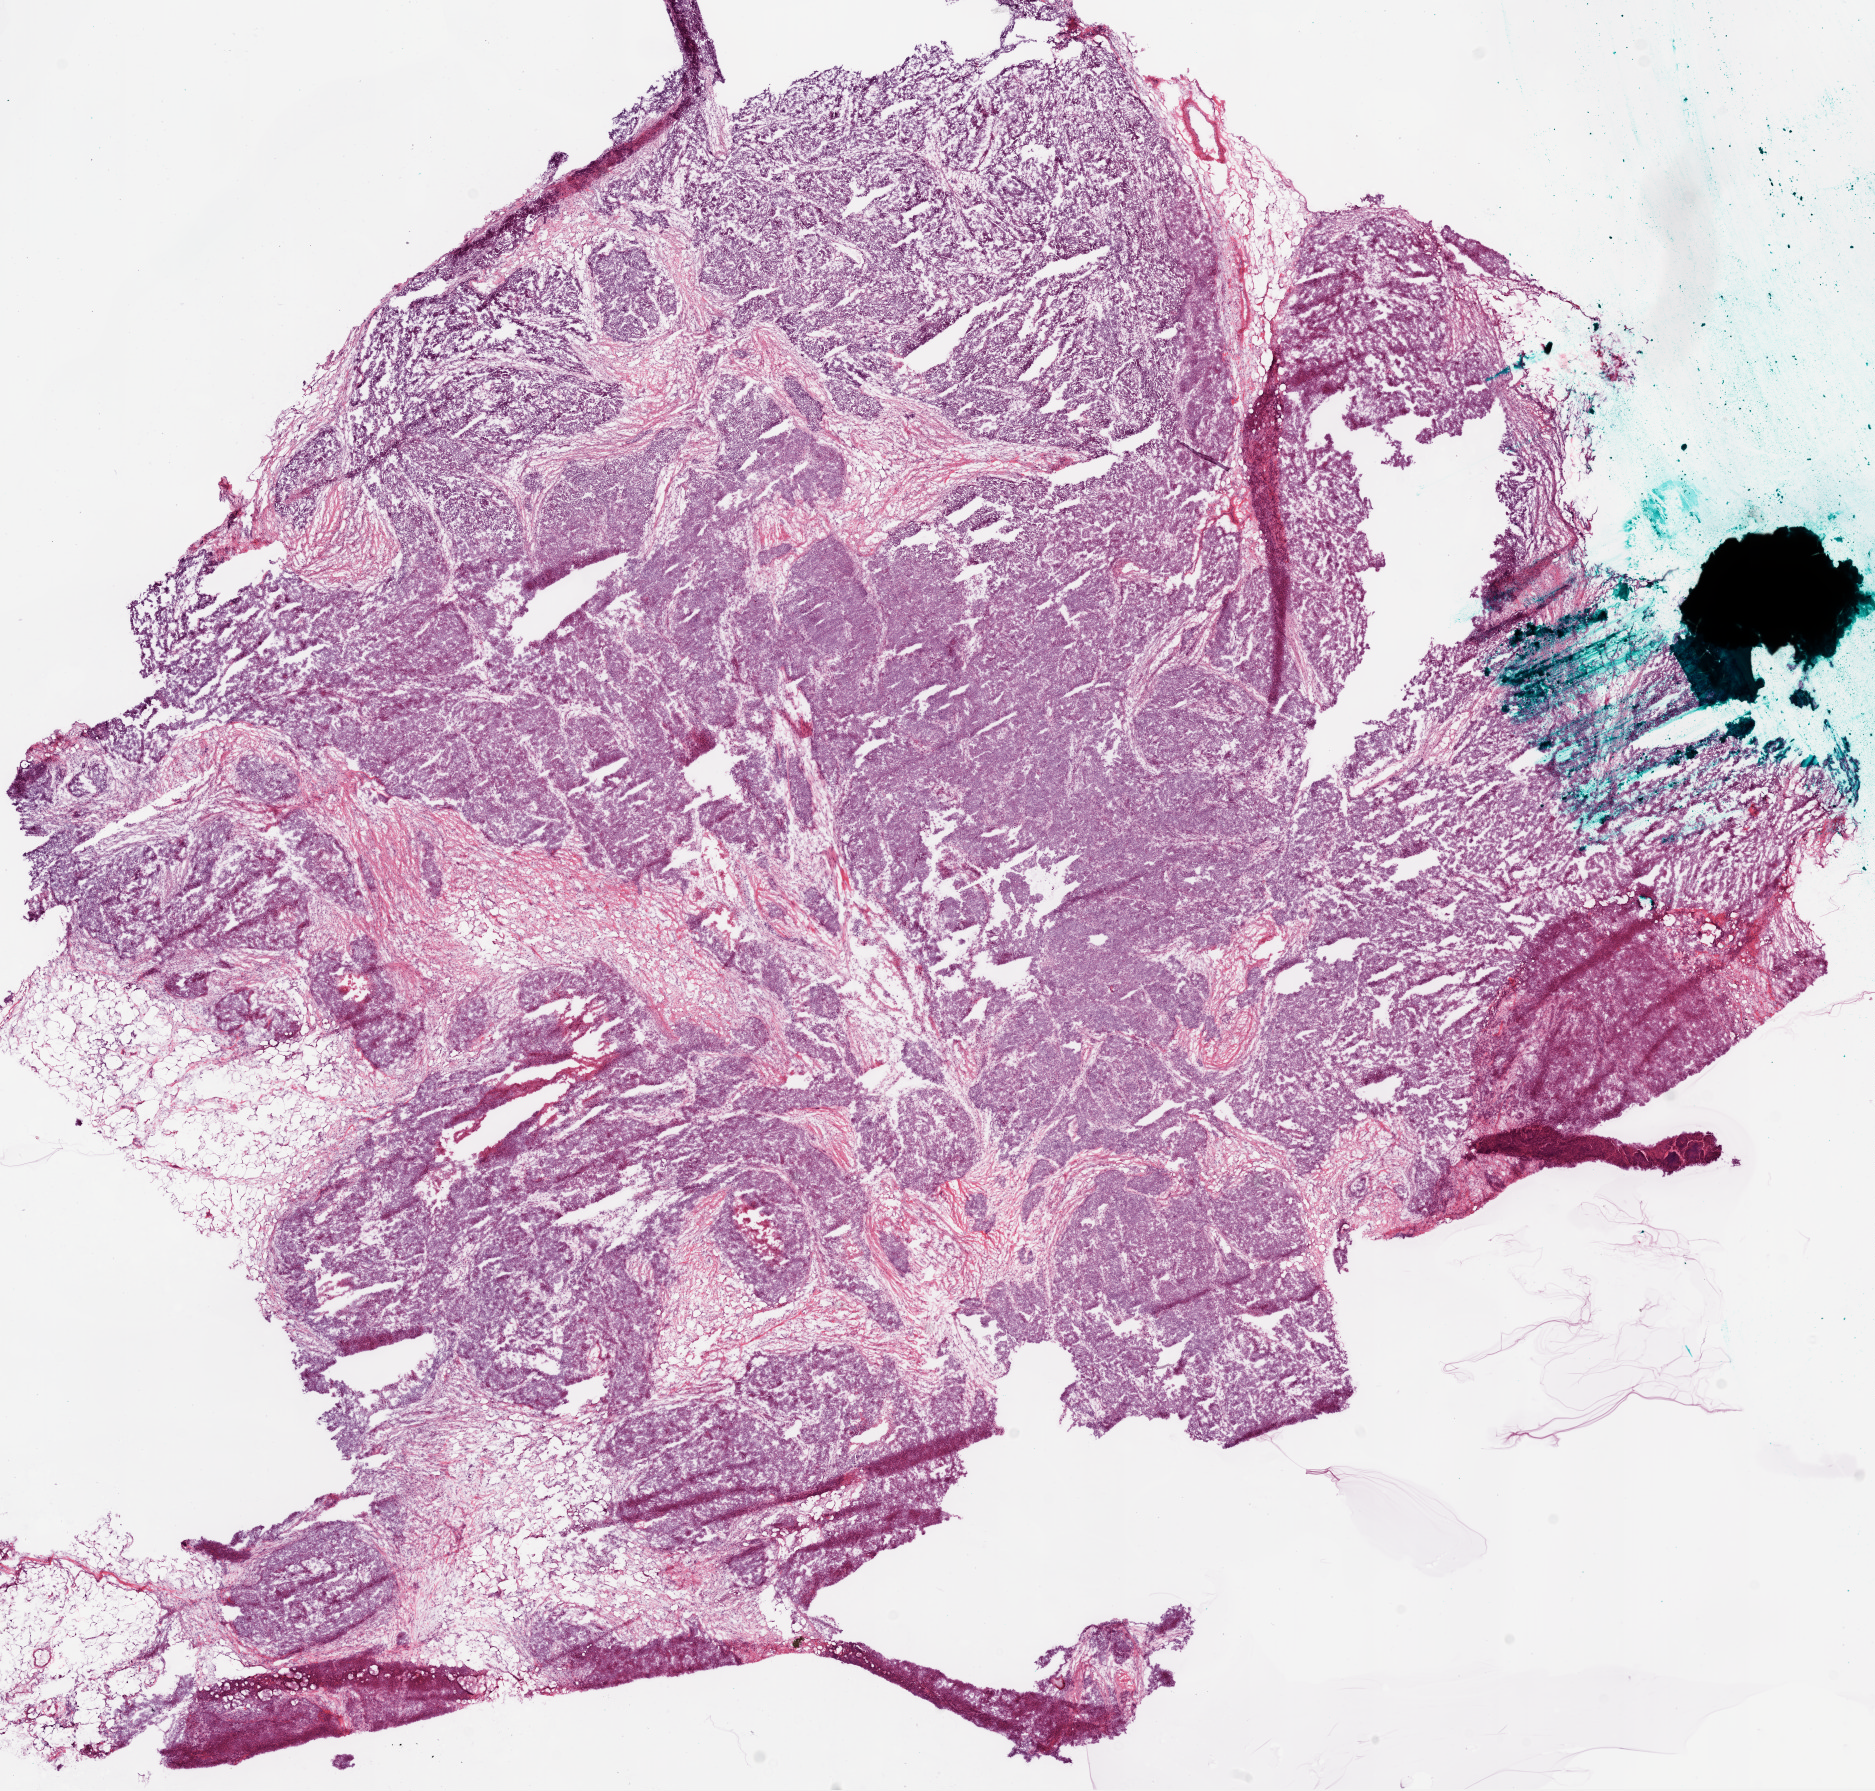
Whole-slide histology image, Hematoxylin and eosin (H&E) stained, shown as a low-resolution overview of the whole scanned area (about 15.0 x 14.4 mm, acquisition: 20x scan). Frozen section from the bottom of the tissue portion. Ovary, primary tumour sample. Patient: female, age at initial diagnosis 70 years. Pathologist review of this section (percent, as recorded): tumour cells 80%, tumour nuclei 80%.
Histologic diagnosis: Serous cystadenocarcinoma, NOS.